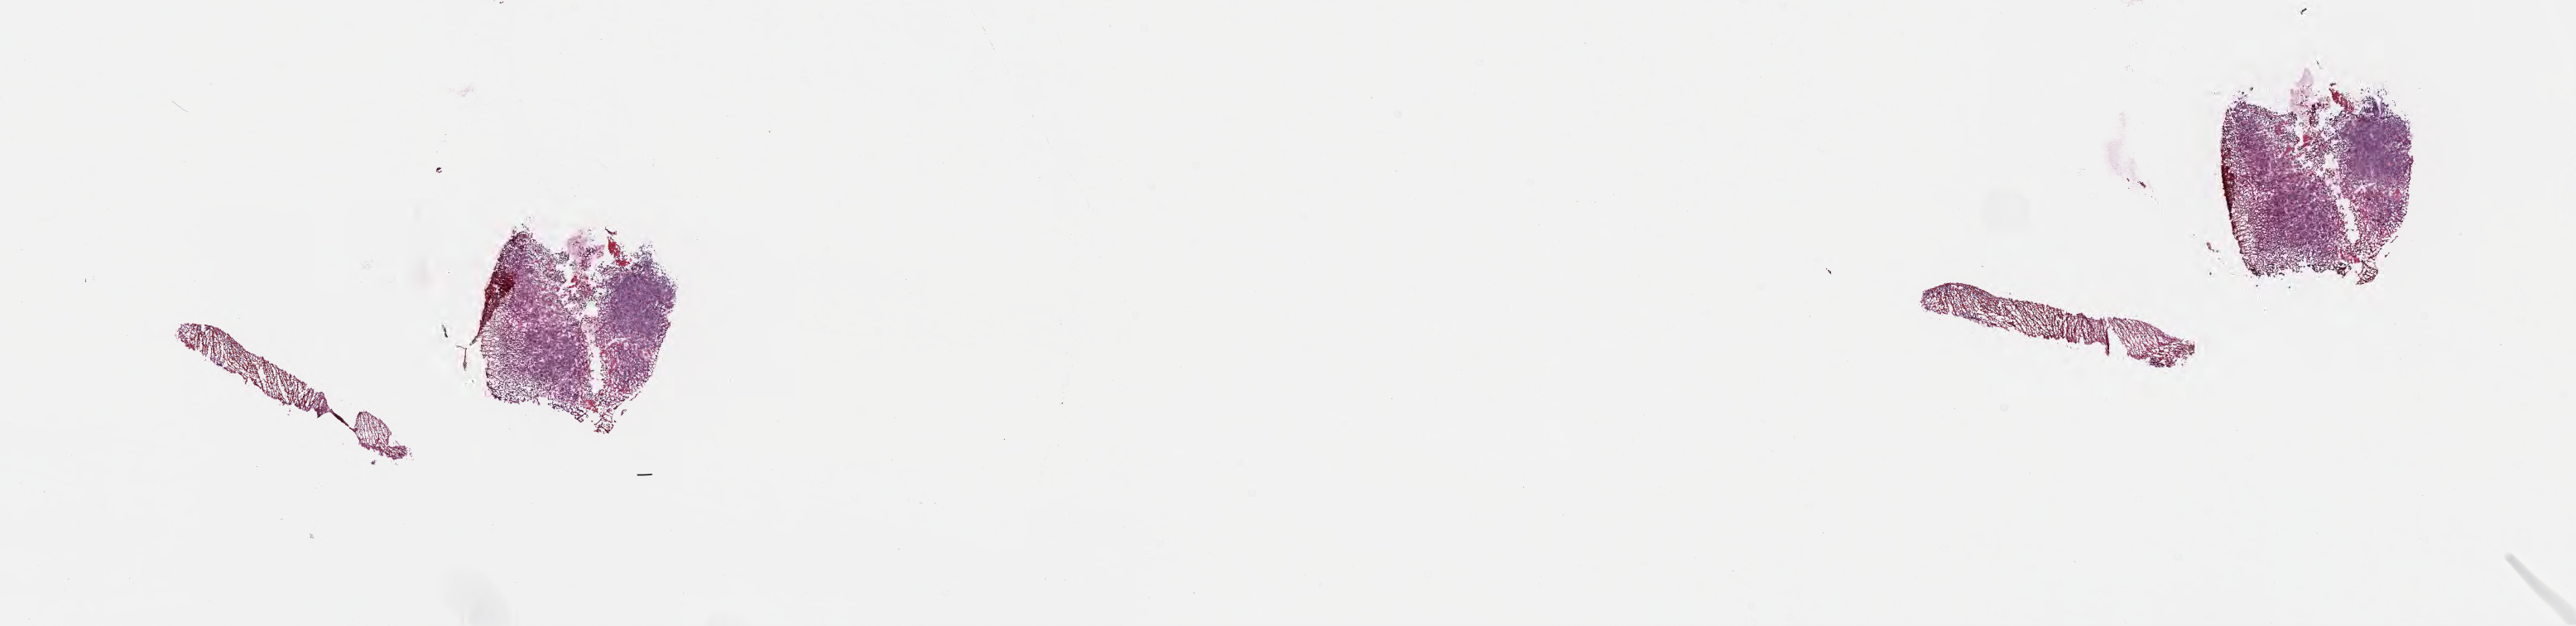
Haematoxylin and eosin whole-slide image — whole scanned area (about 25.2 x 6.1 mm) shown as a low-resolution overview. Frozen section. Specimen: primary tumor. Anatomic site: pelvis. Patient: female, age at initial diagnosis 7 years. Slide review estimates, as recorded: tumor cells 60%, tumor nuclei 70%, stromal cells 20%, necrosis 15%, normal cells 5%. Inflammatory infiltration, as recorded: lymphocyte infiltration 70%, monocyte infiltration 15%, neutrophil infiltration 5%.
Ann Arbor stage (patient): Stage III. Section: top of the tissue portion. Histologic diagnosis: Burkitt lymphoma, NOS.